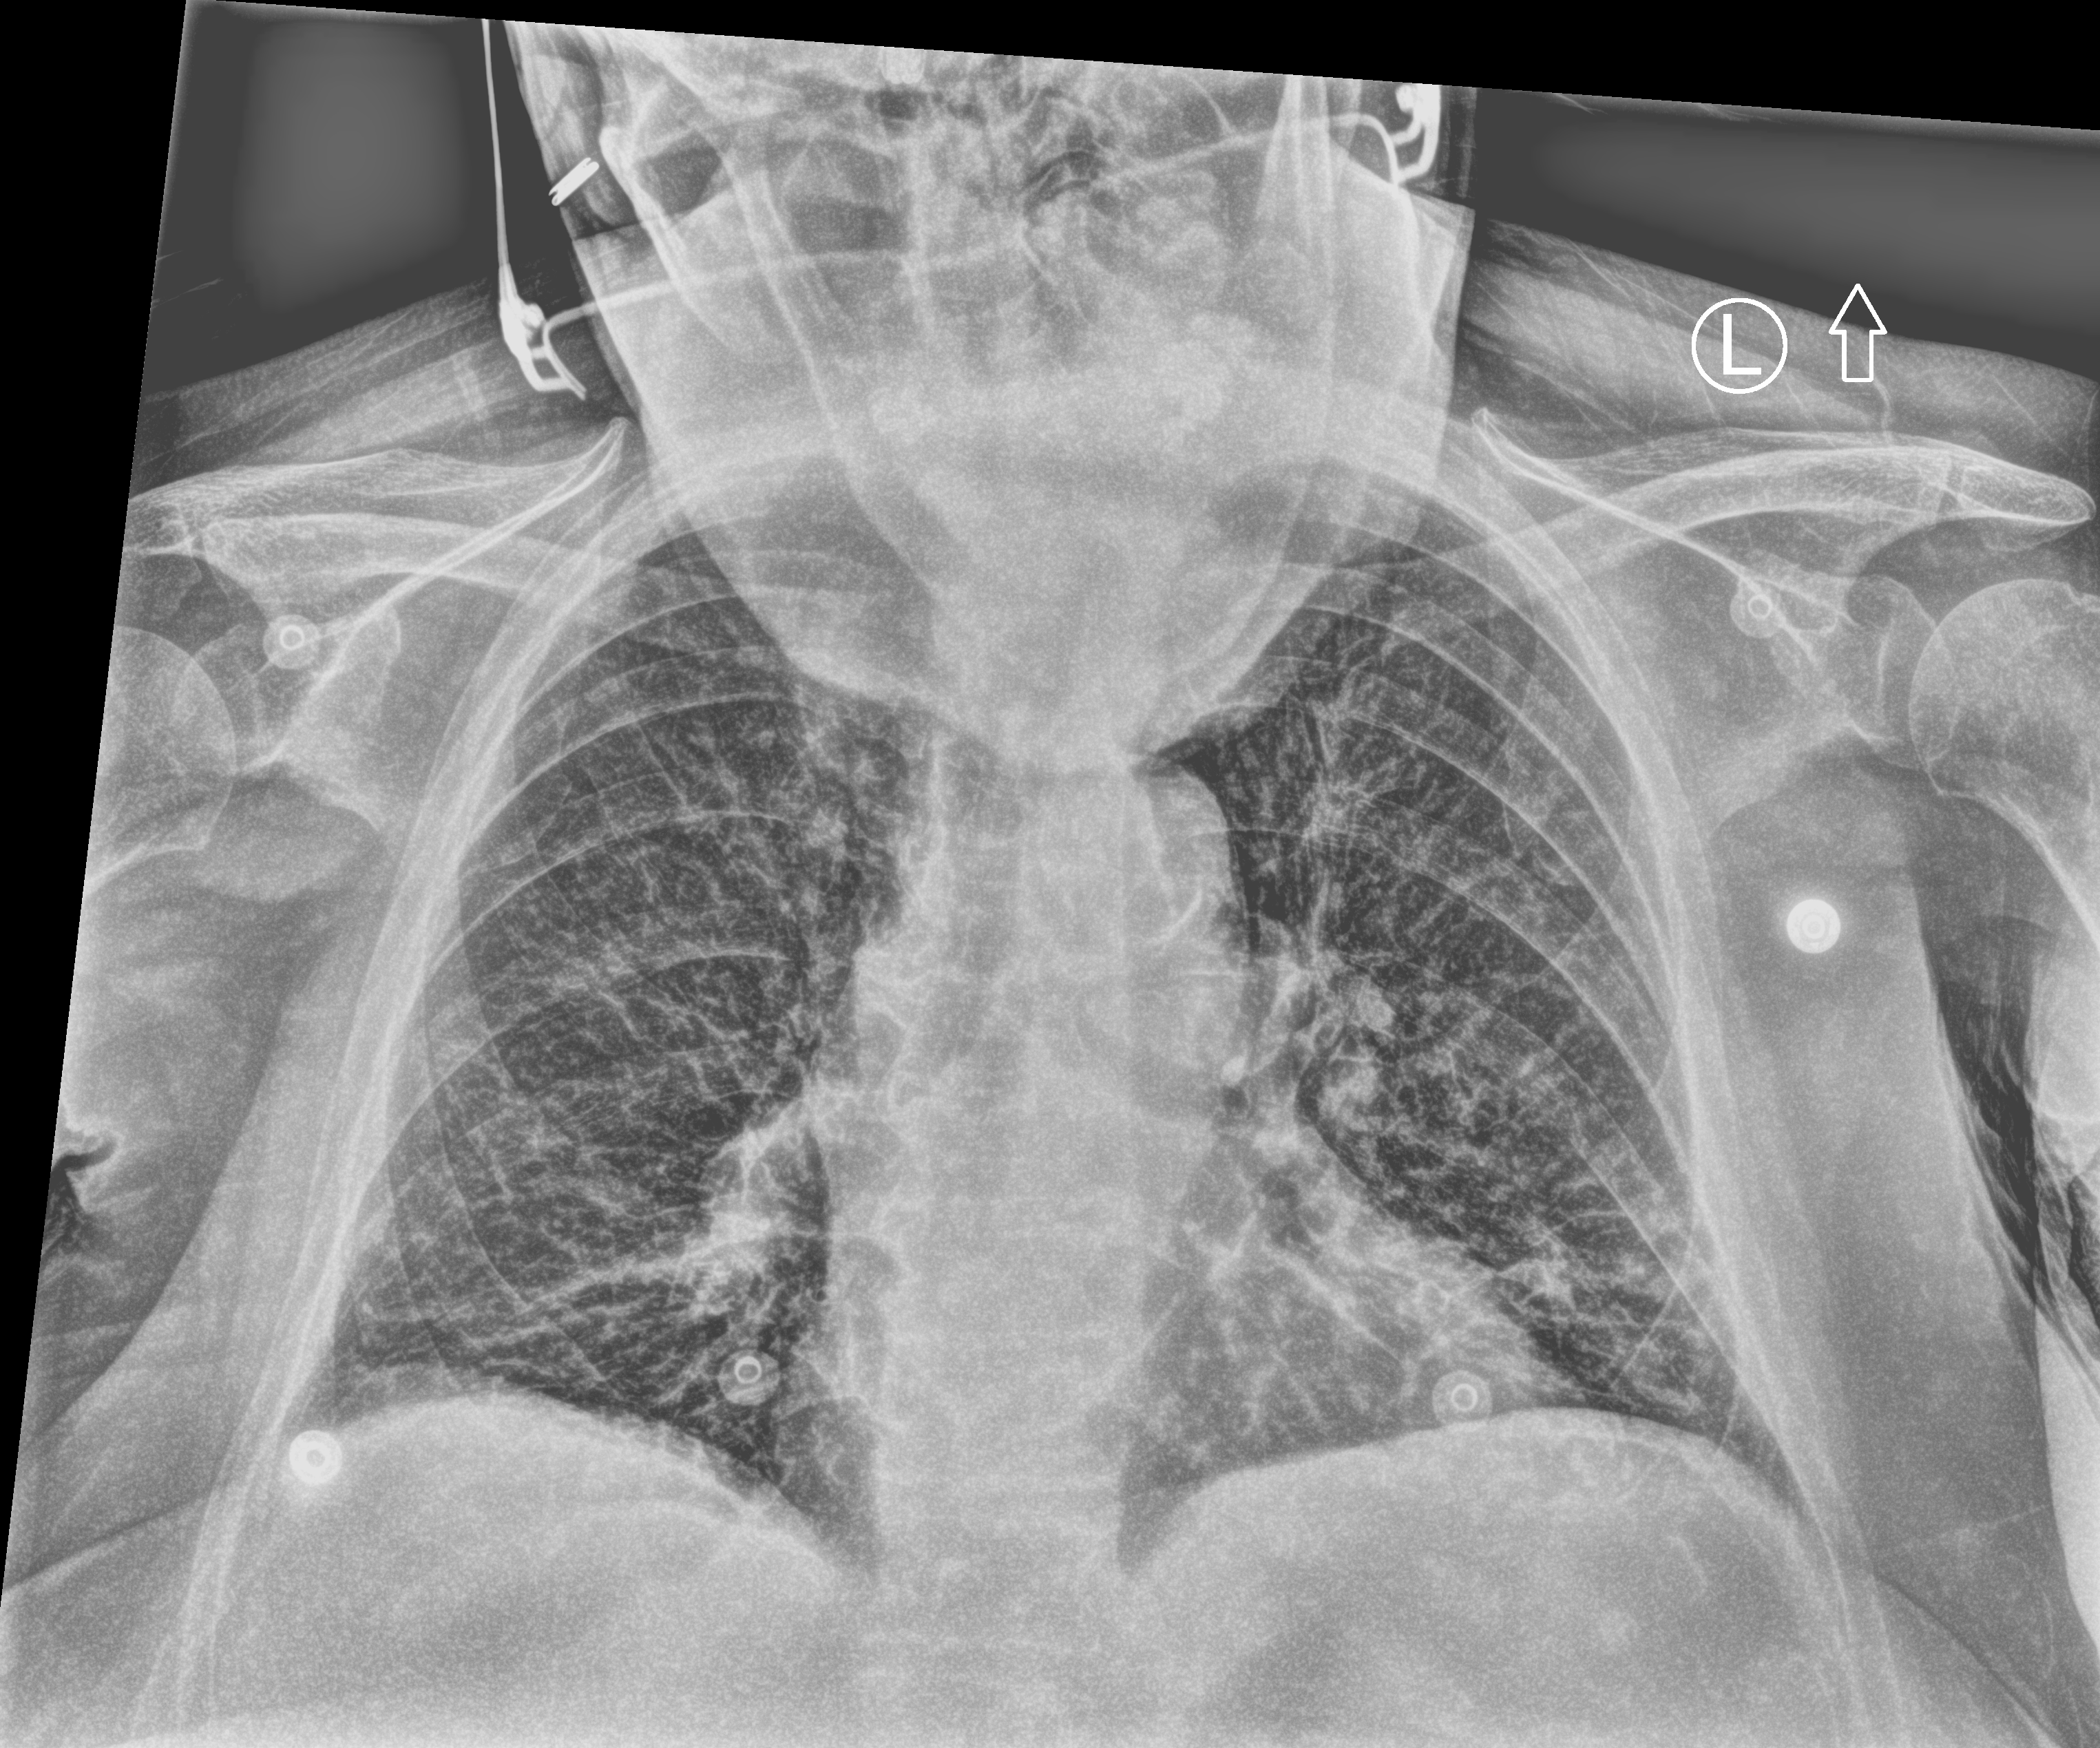
Chest X-ray (portable); anteroposterior (AP) projection. Patient hospitalised with COVID-19; female, aged 75–90 years.
Hospital-stay facts (about this admission, not read from this image; timing relative to this image not recorded): smoking status (admission record): former; admitted to intensive care during this hospital stay: no; length of hospital stay: 19 days.